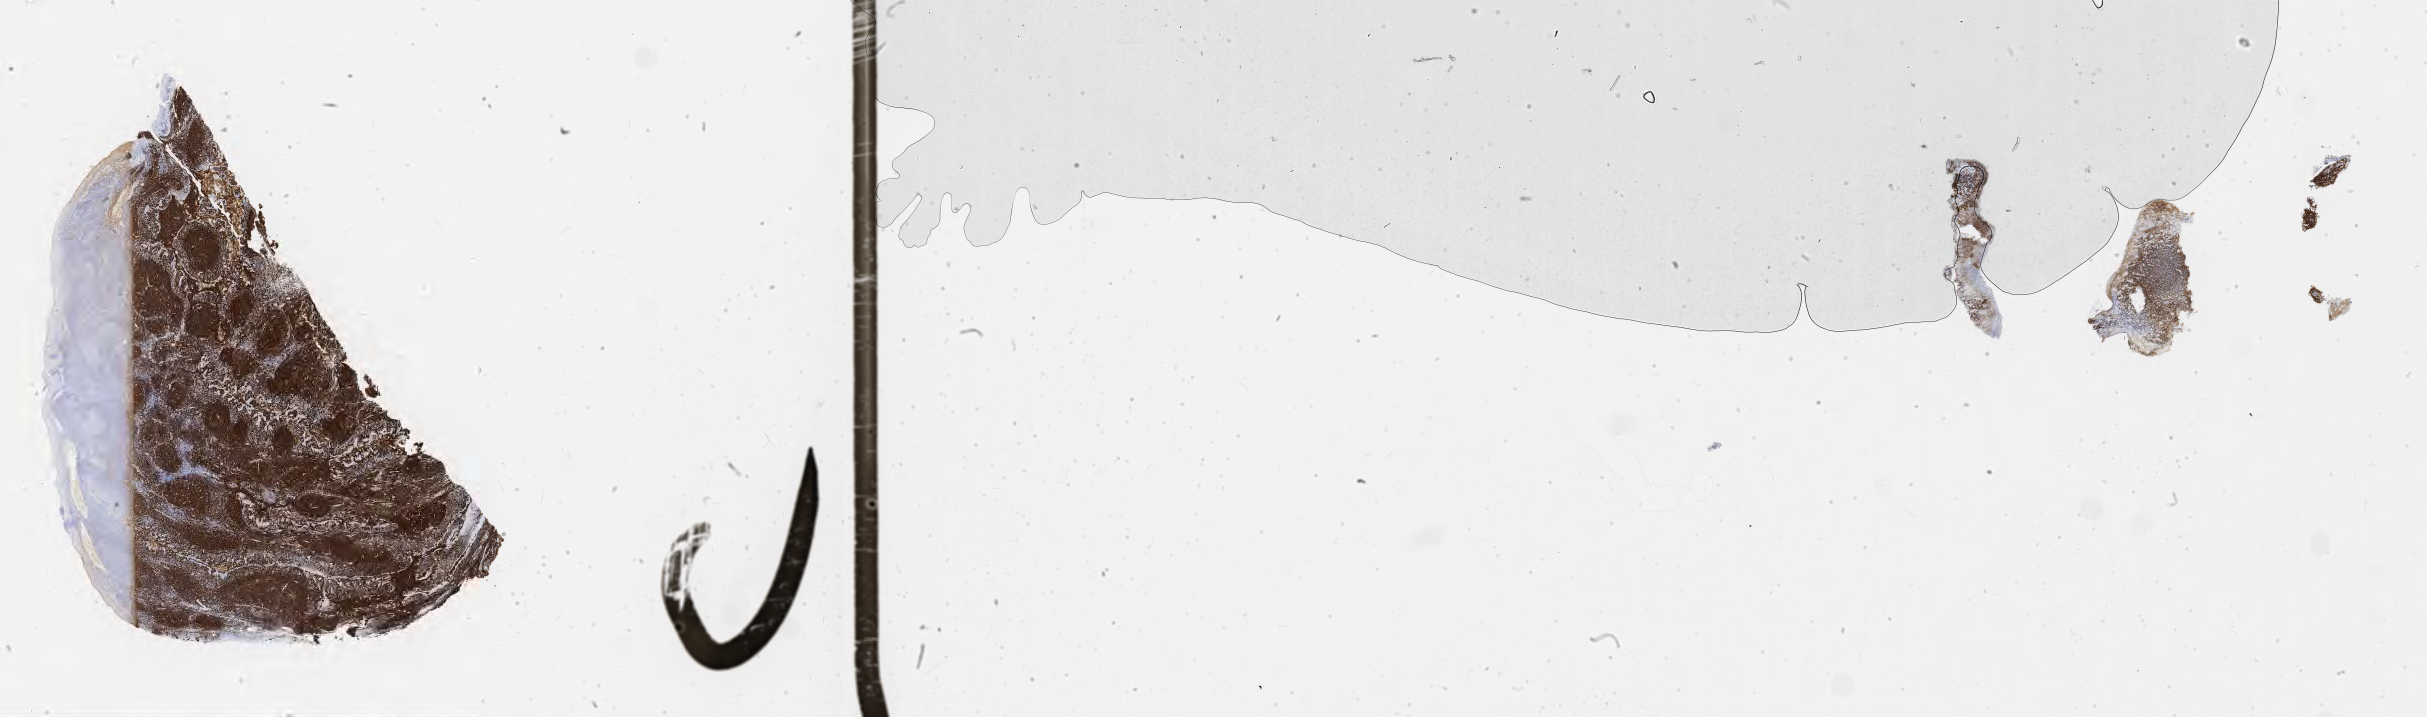
Whole-slide image, immunohistochemical stain for CD20 — shown as a low-resolution overview of the whole scanned area (about 39.2 x 11.6 mm). Tumor tissue. Site: colon. Patient male; aged 28.
Histologic diagnosis: Burkitt lymphoma, NOS.